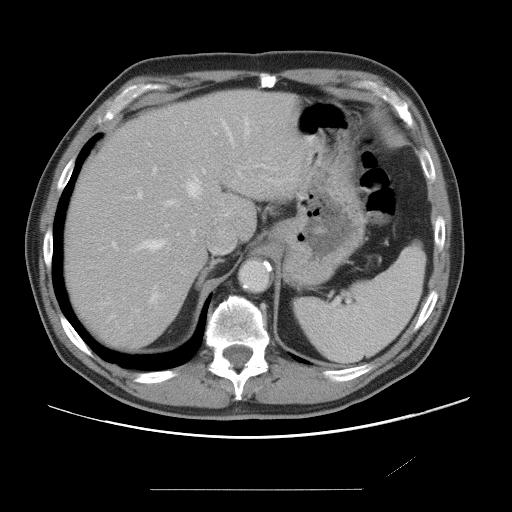
Contrast-enhanced abdominal CT, one axial slice; intravenous contrast given; soft-tissue window (W 400 / L 40 HU); 5 mm slice thickness; 512 × 512 image matrix. Male patient, age 74 years. From the clinical record (not read from this slice): diagnosis: colorectal cancer liver metastases, imaged before liver resection; multiple liver metastases: yes; largest metastasis: 1.1 cm.
Structures marked on this image (expert manual segmentation):
- hepatic veins: bounding box (x1, y1, x2, y2) in pixels: (139, 121, 251, 302)
- liver: (65, 91, 302, 351)
- planned liver remnant (the part of the liver to remain after resection): (65, 91, 302, 351)
- portal vein (with intrahepatic branches): (112, 168, 206, 247)